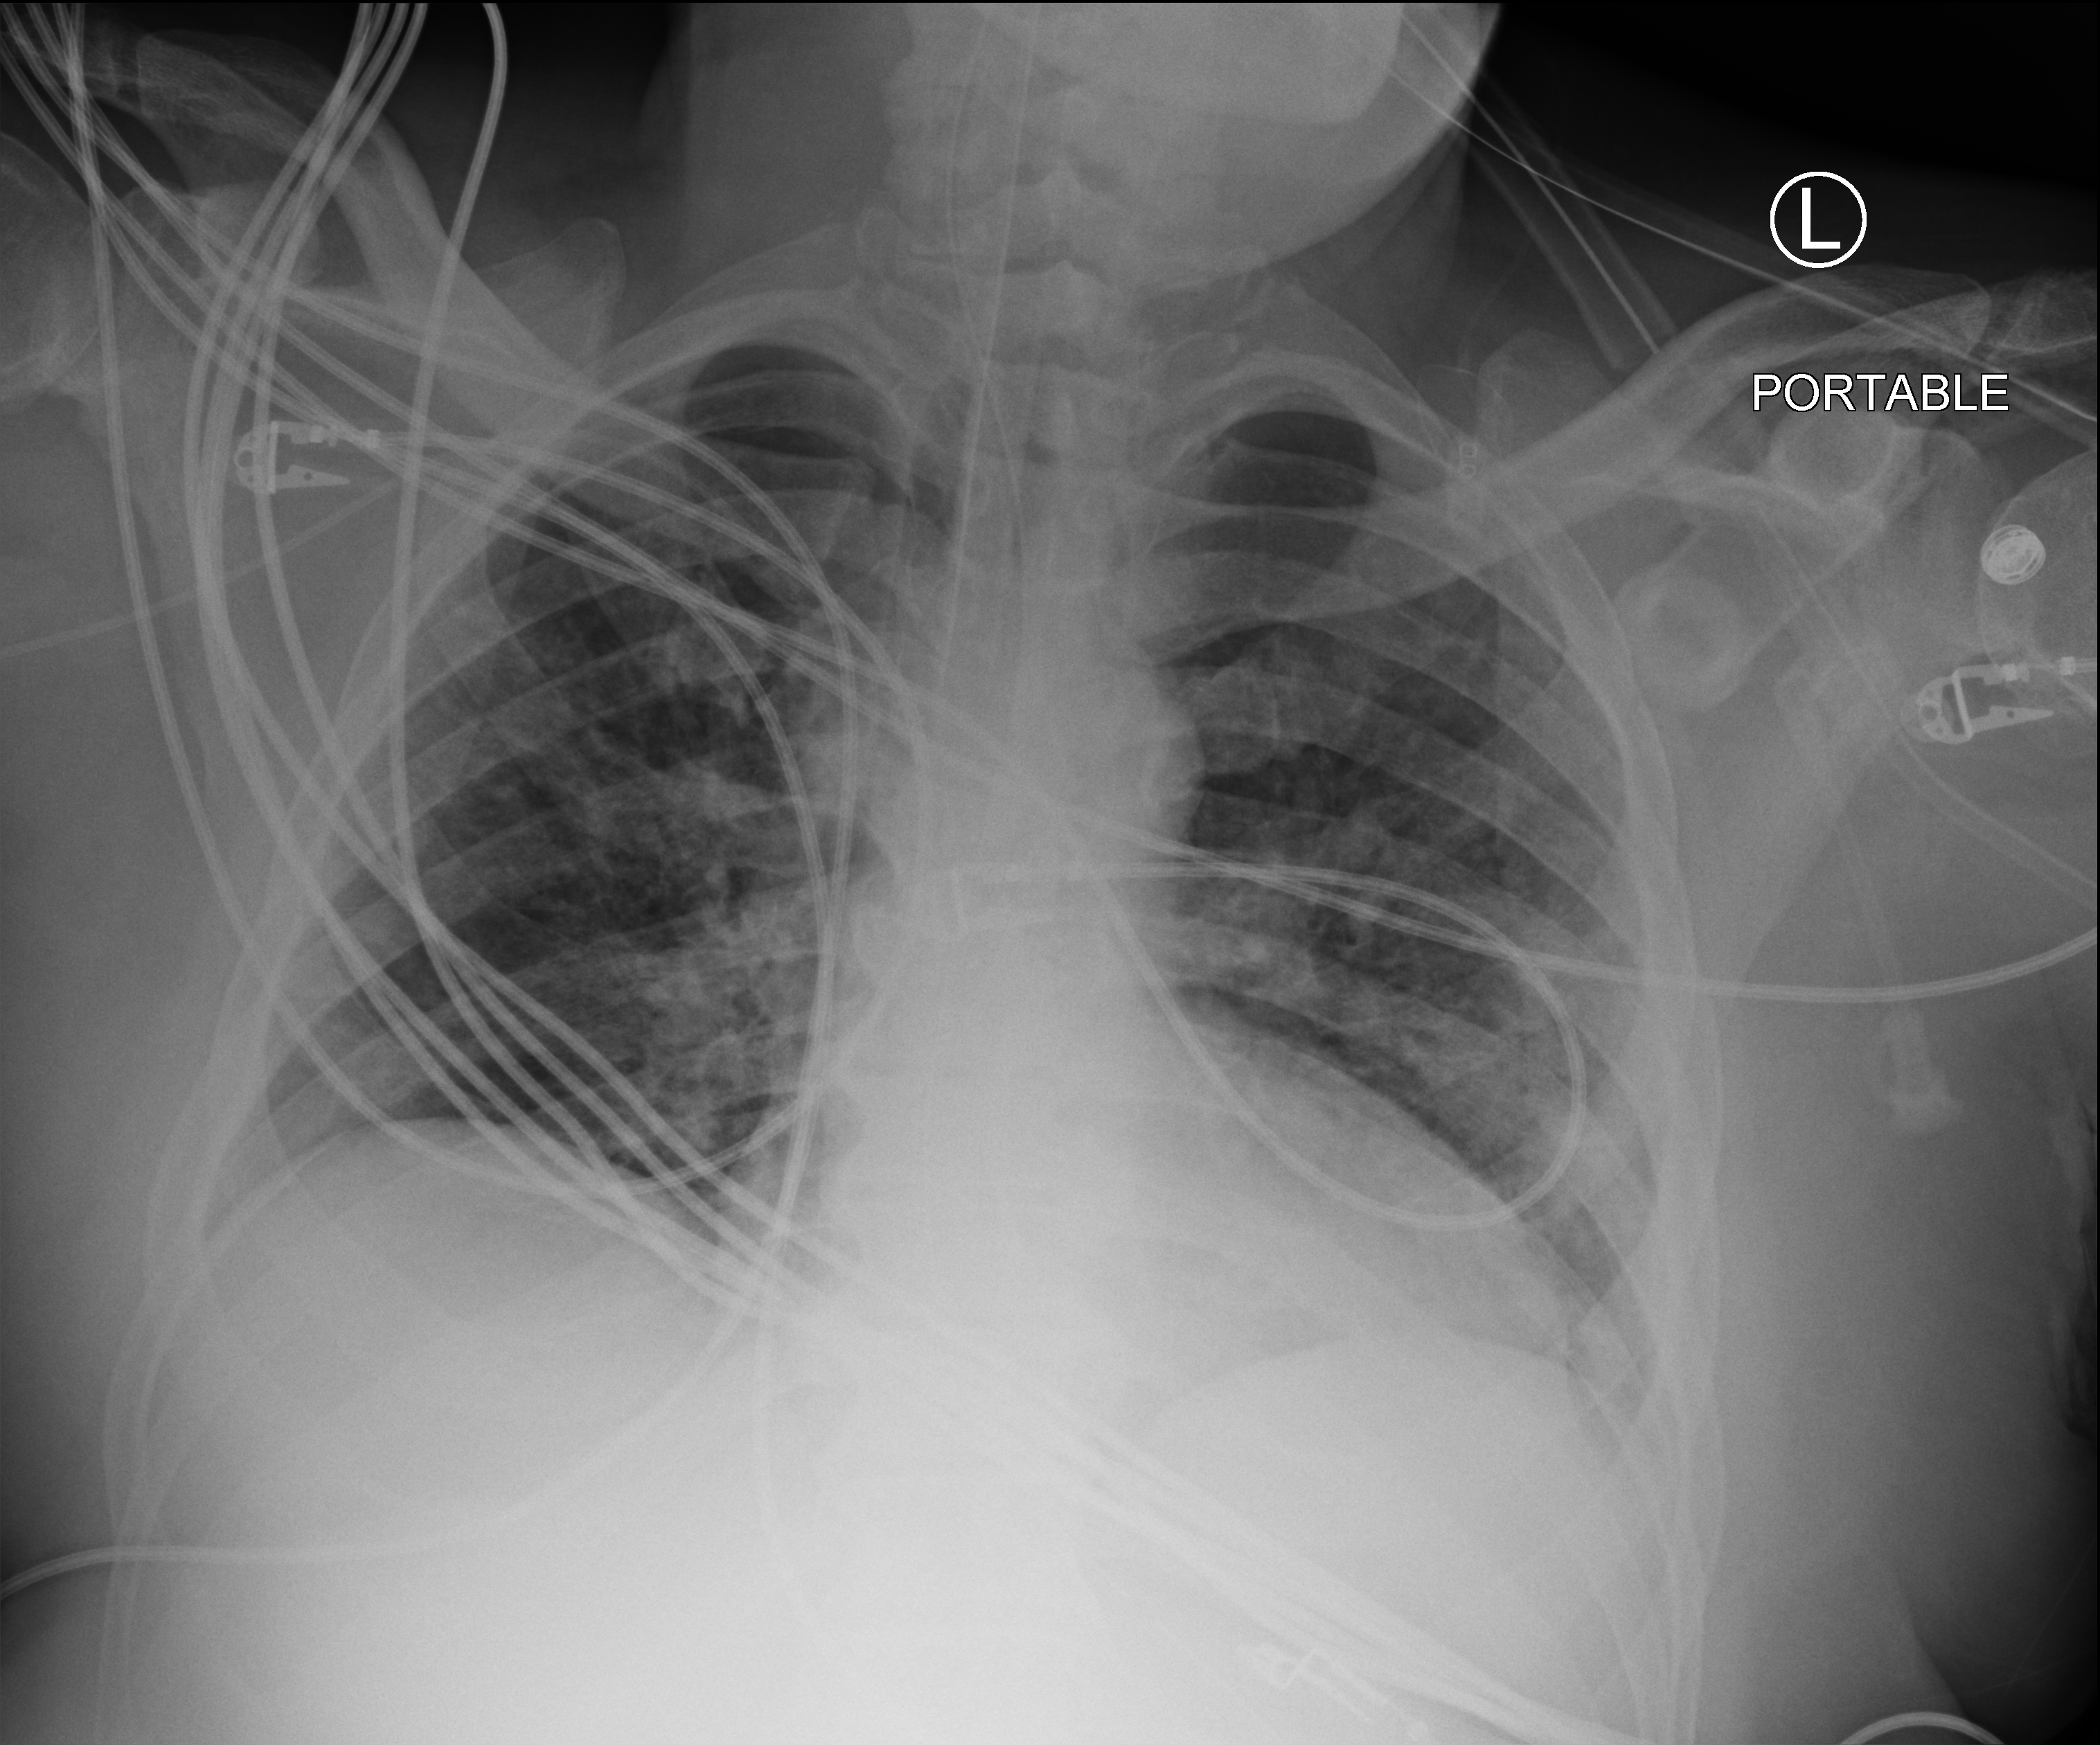
Bedside chest radiograph (computed radiography). Patient hospitalised with COVID-19; male, aged 18–59 years.
From the hospital-stay record, not from the radiograph (when in the stay this image was taken is not recorded): admitted to intensive care during this hospital stay: yes.